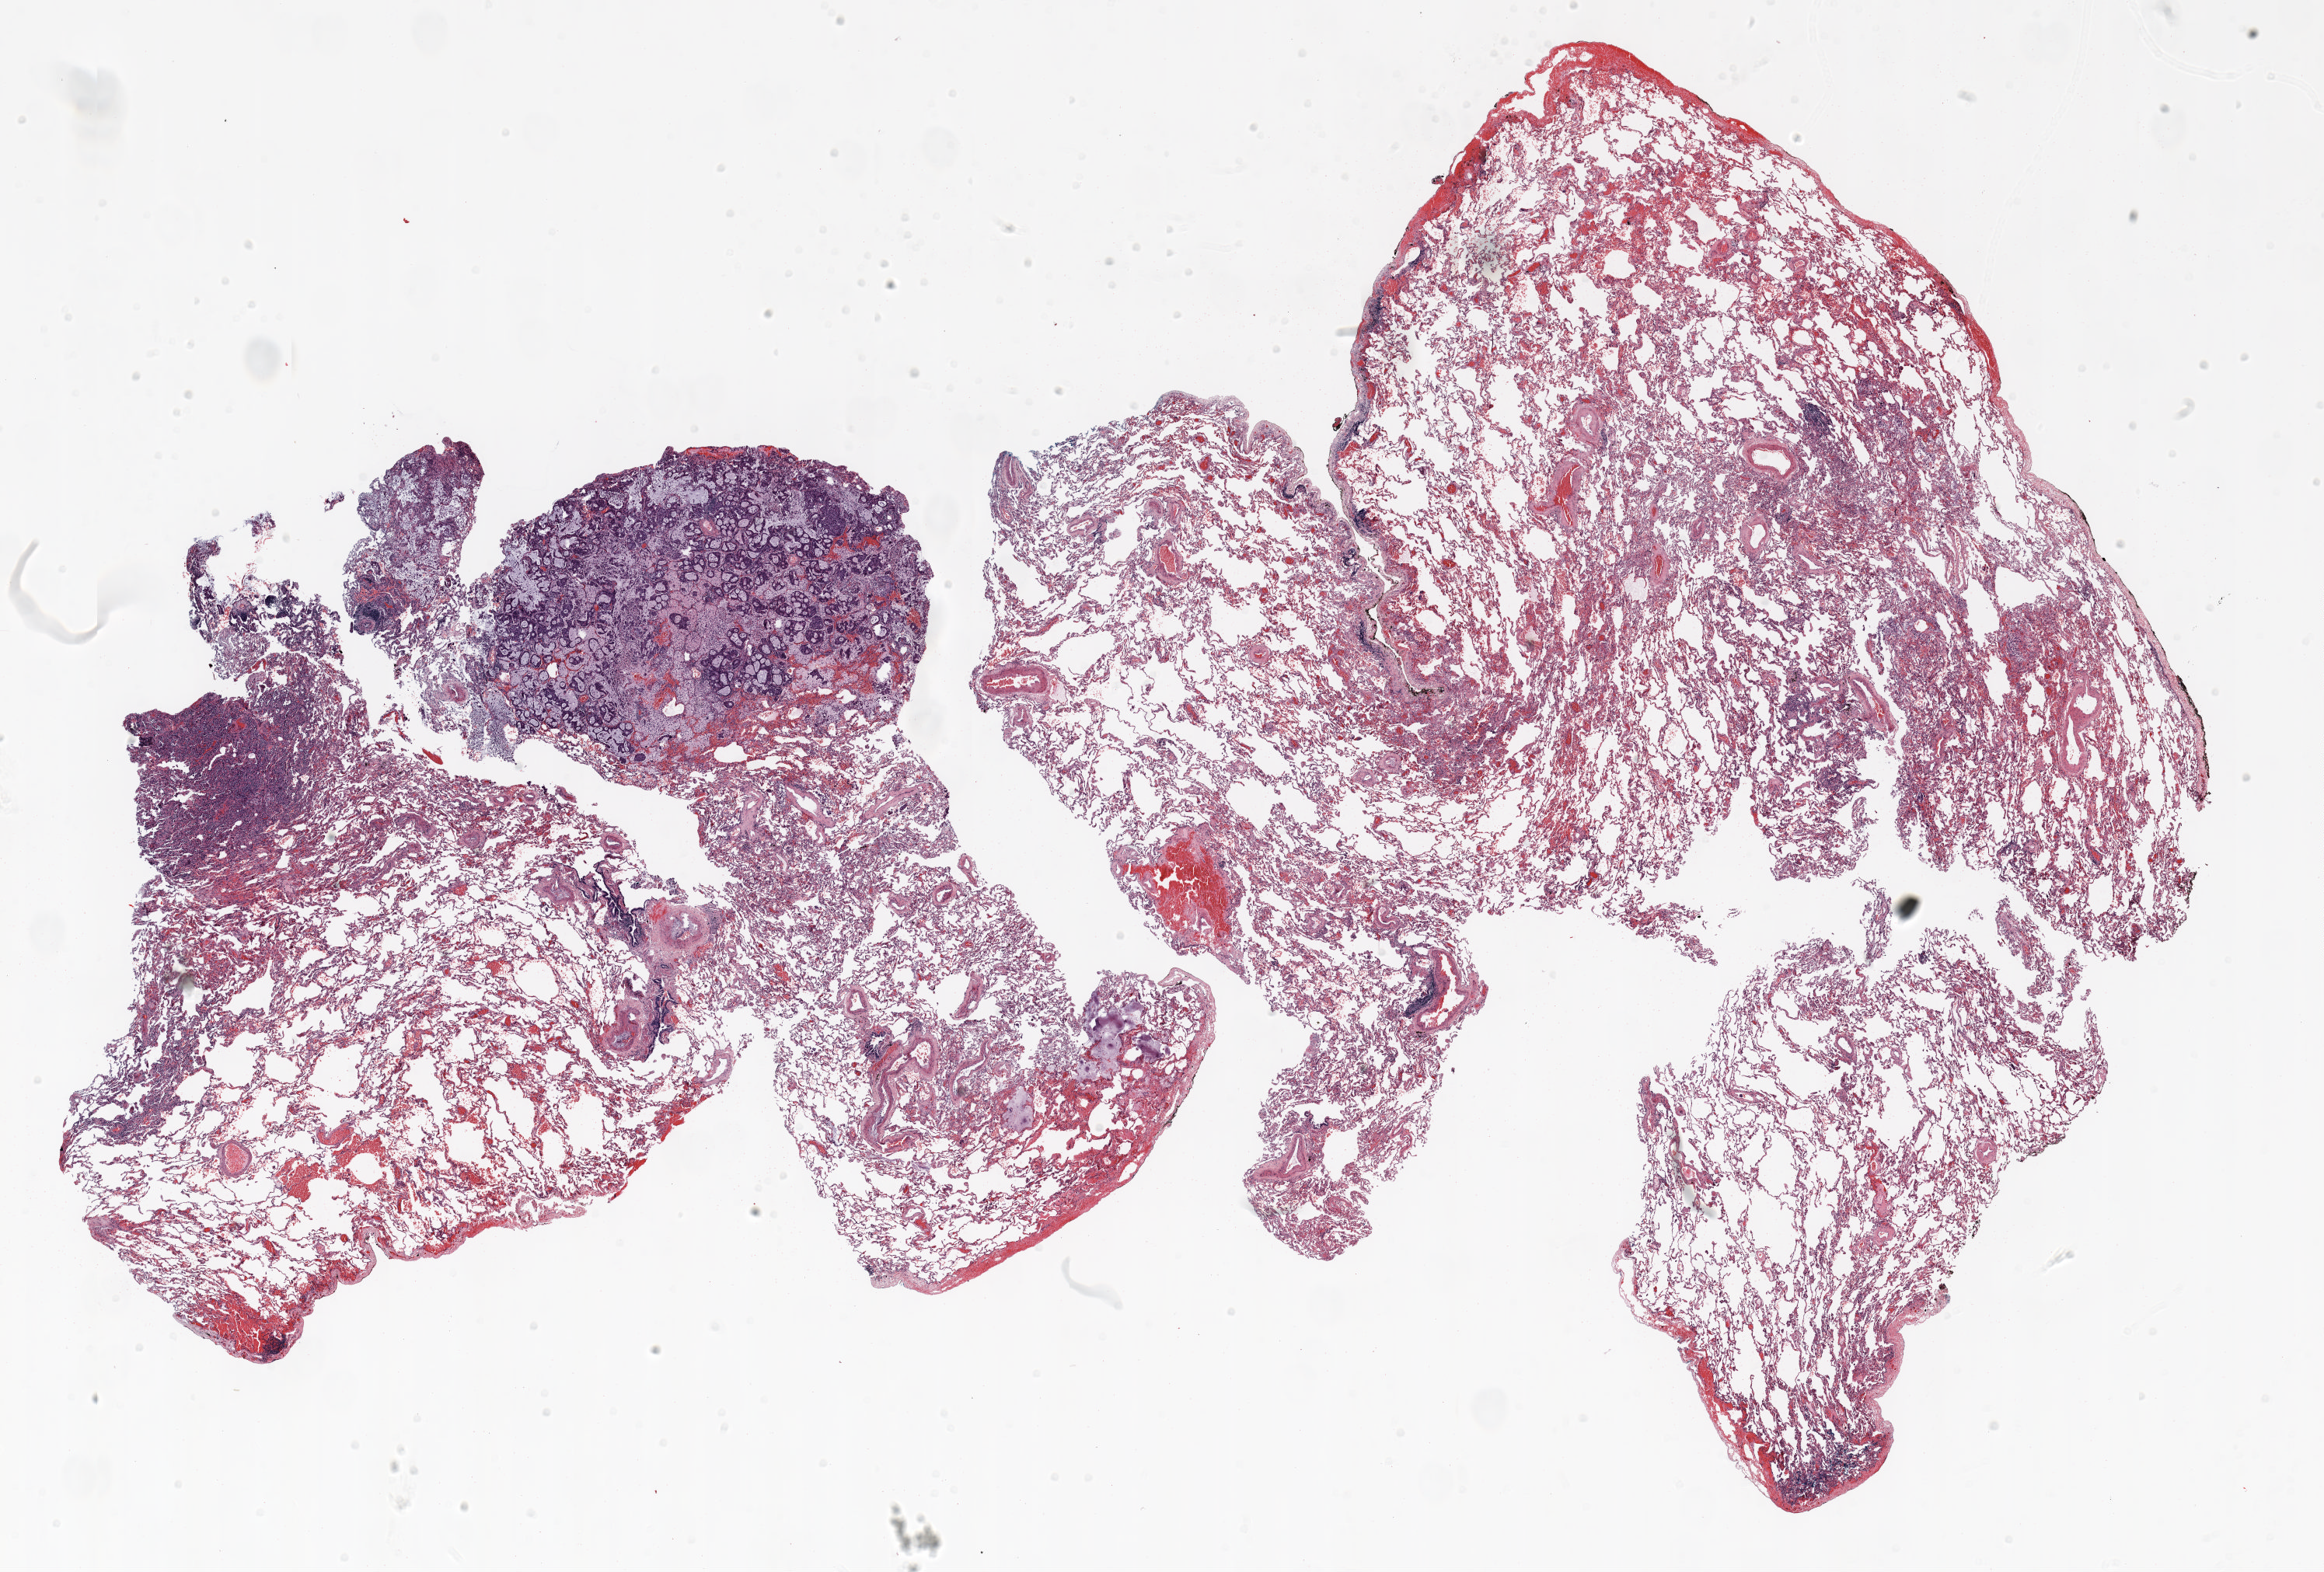
Whole-slide histology image, H&E-stained — low-resolution overview of the scanned area, about 24.0 x 16.3 mm (slide scanned at 20x), FFPE section, lung. Male, age 59 at enrolment. Former smoker at enrolment. Grade: poorly differentiated (G3).
Tumour size (pathology): 21 mm. Participant's lung-cancer diagnosis: Signet ring cell carcinoma (ICD-O-3 8490/3). Stage (AJCC 6th edition): IIIA. Primary tumour location (clinical record): left lower lobe.